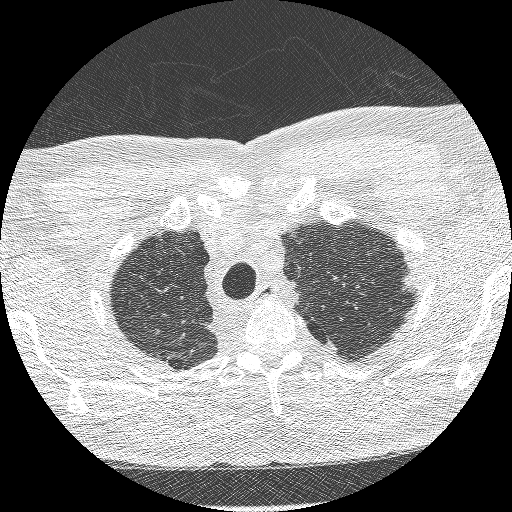
Axial slice from a low-dose chest CT screening exam, third screening round (two years after baseline), lung window (W 1500 / L -600 HU), lung (sharp) reconstruction kernel (BONE), 120 kVp, slice 242 of 275 in the series. Male, age 66 years at enrolment. Current smoker at enrolment.
Lesion marked by an expert reader, bounding box (x1, y1, x2, y2) in pixels: (385, 268, 431, 317). The exam's reader record, not a measurement of the box and not confirmed to be the same lesion: non-calcified nodule or mass ≥4 mm, left lower lobe, 15 × 9 mm, spiculated (stellate) margins, soft tissue attenuation, pre-existing on the prior screen: yes; interval growth: yes. Later outcome: lung cancer diagnosed 225 days after this screen — adenocarcinoma, NOS, left upper lobe, poorly differentiated (G3), stage IB (AJCC 6th edition), 16 mm at pathology.